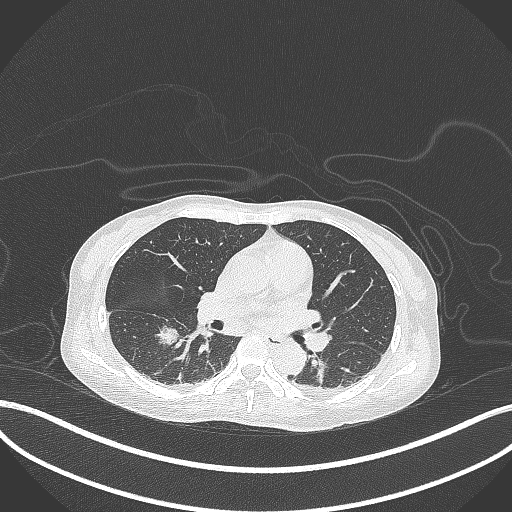
Chest CT, one axial slice; slice 165 of 261 in the series (ordered by position); 120 kVp; lung window (W 1500 / L -600 HU); 512 × 512 image matrix, field of view 400 × 400 mm. Patient: female, 44 years. Case-level facts recorded for this patient, not image findings: clinical TNM (as recorded): T1c N0 M0.
Structures marked on this image (bounding box drawn by a radiologist):
- lung tumour (recorded histology: adenocarcinoma): box from (x=152, y=323) to (x=180, y=351) px